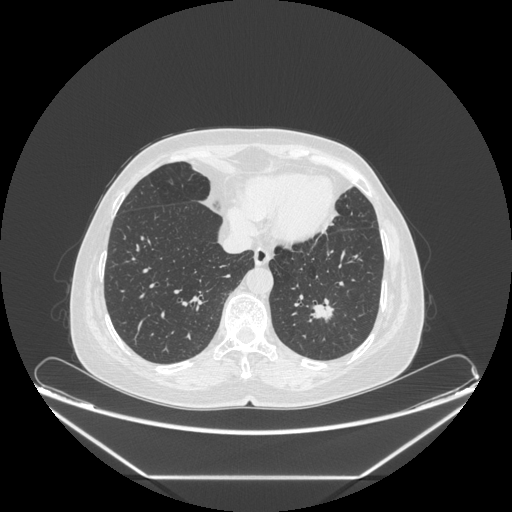
Chest CT, one axial slice; slice 72 of 241 in the series (ordered by position); reconstruction kernel STANDARD; 120 kVp; lung window (W 1500 / L -600 HU); 512 × 512 image matrix, field of view 451 × 451 mm. Female patient, age 63 years. Case-level facts recorded for this patient, not image findings: clinical TNM (as recorded): T1c N0 M0.
Annotated regions visible in this slice (bounding box drawn by a radiologist):
- lung tumour (recorded histology: adenocarcinoma): box from (x=306, y=295) to (x=348, y=338) px